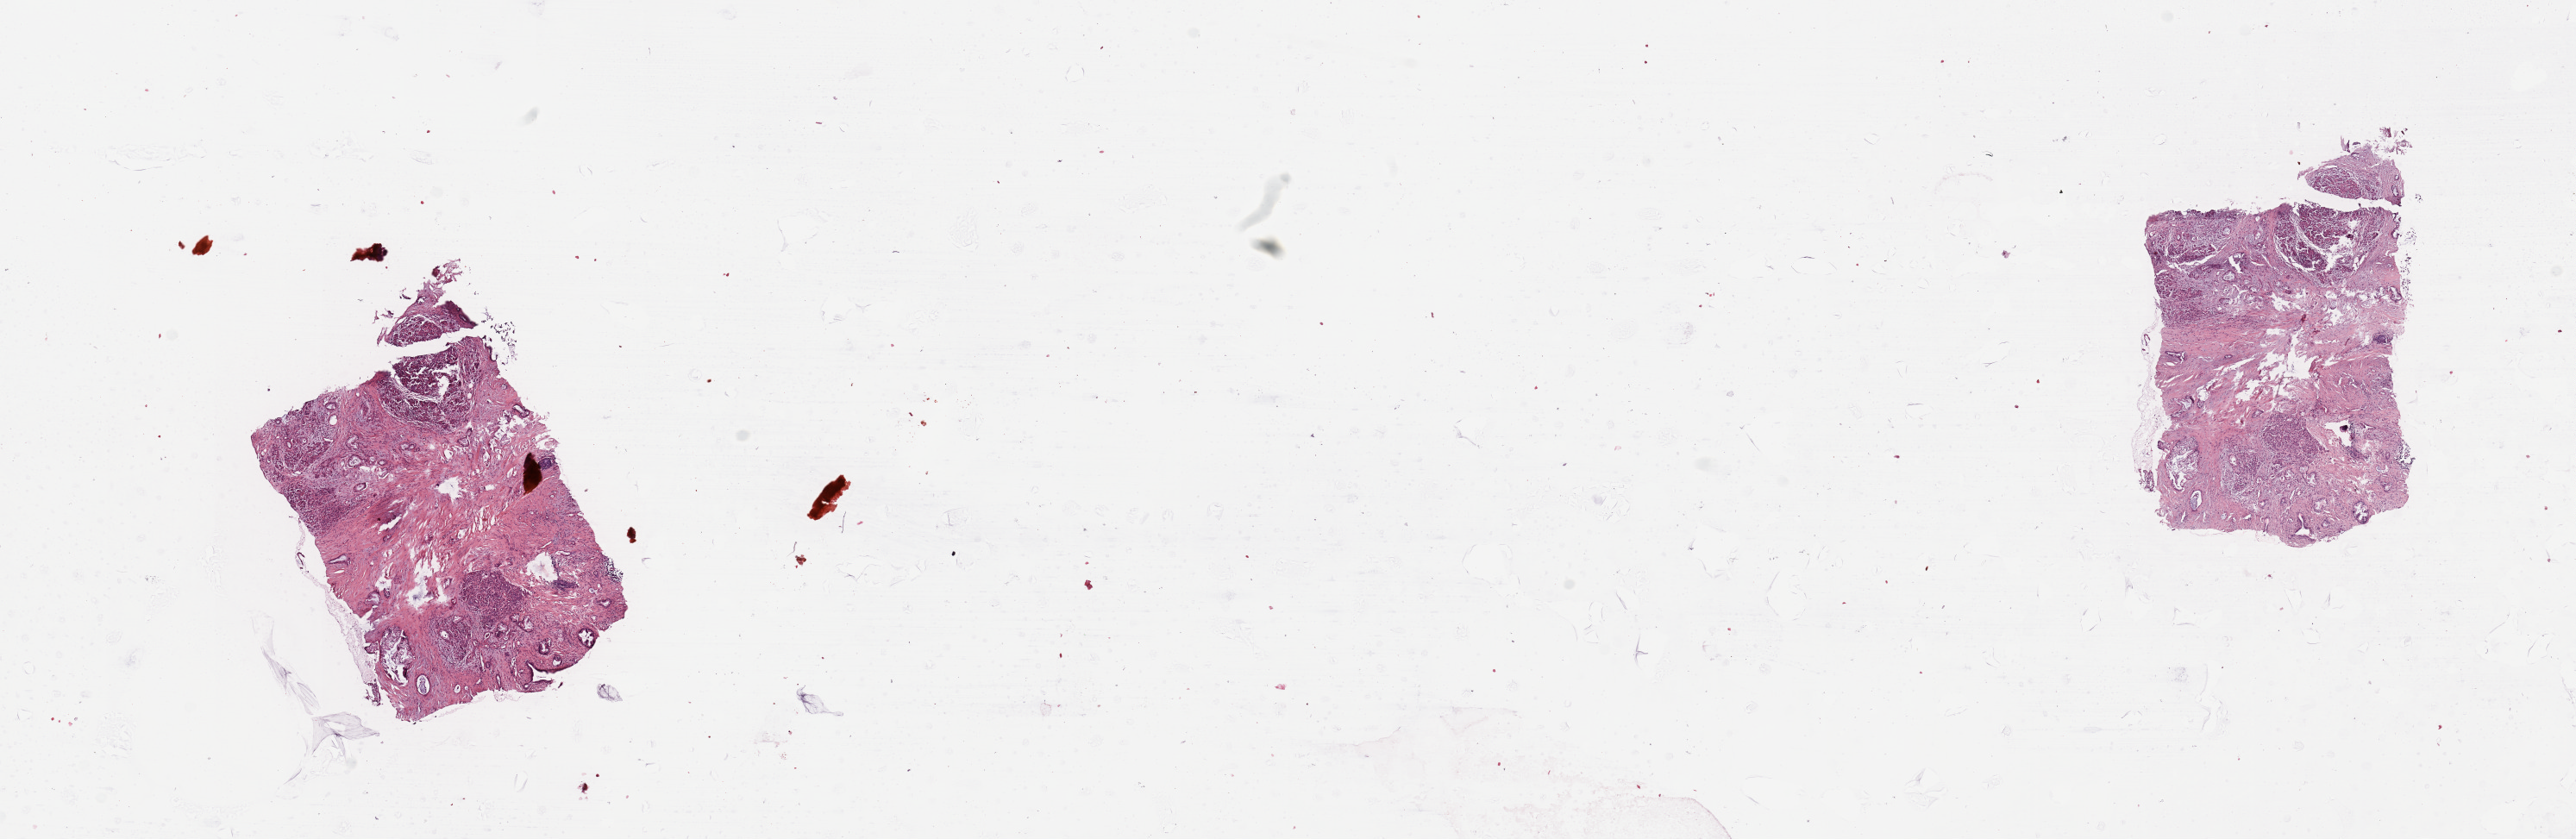
Whole-slide histology image, H&E-stained, whole scanned area (about 23.6 x 7.7 mm) shown as a low-resolution overview, tumour tissue sample, sampled site: pancreas. Female, 62 y/o. Histologic grade: G2 (moderately differentiated). Composition of this section per pathologist review: tumour nuclei 10%, necrosis 3%.
Diagnosis: Infiltrating duct carcinoma, NOS. AJCC pathologic stage: III. Primary tumour site (as recorded): head.